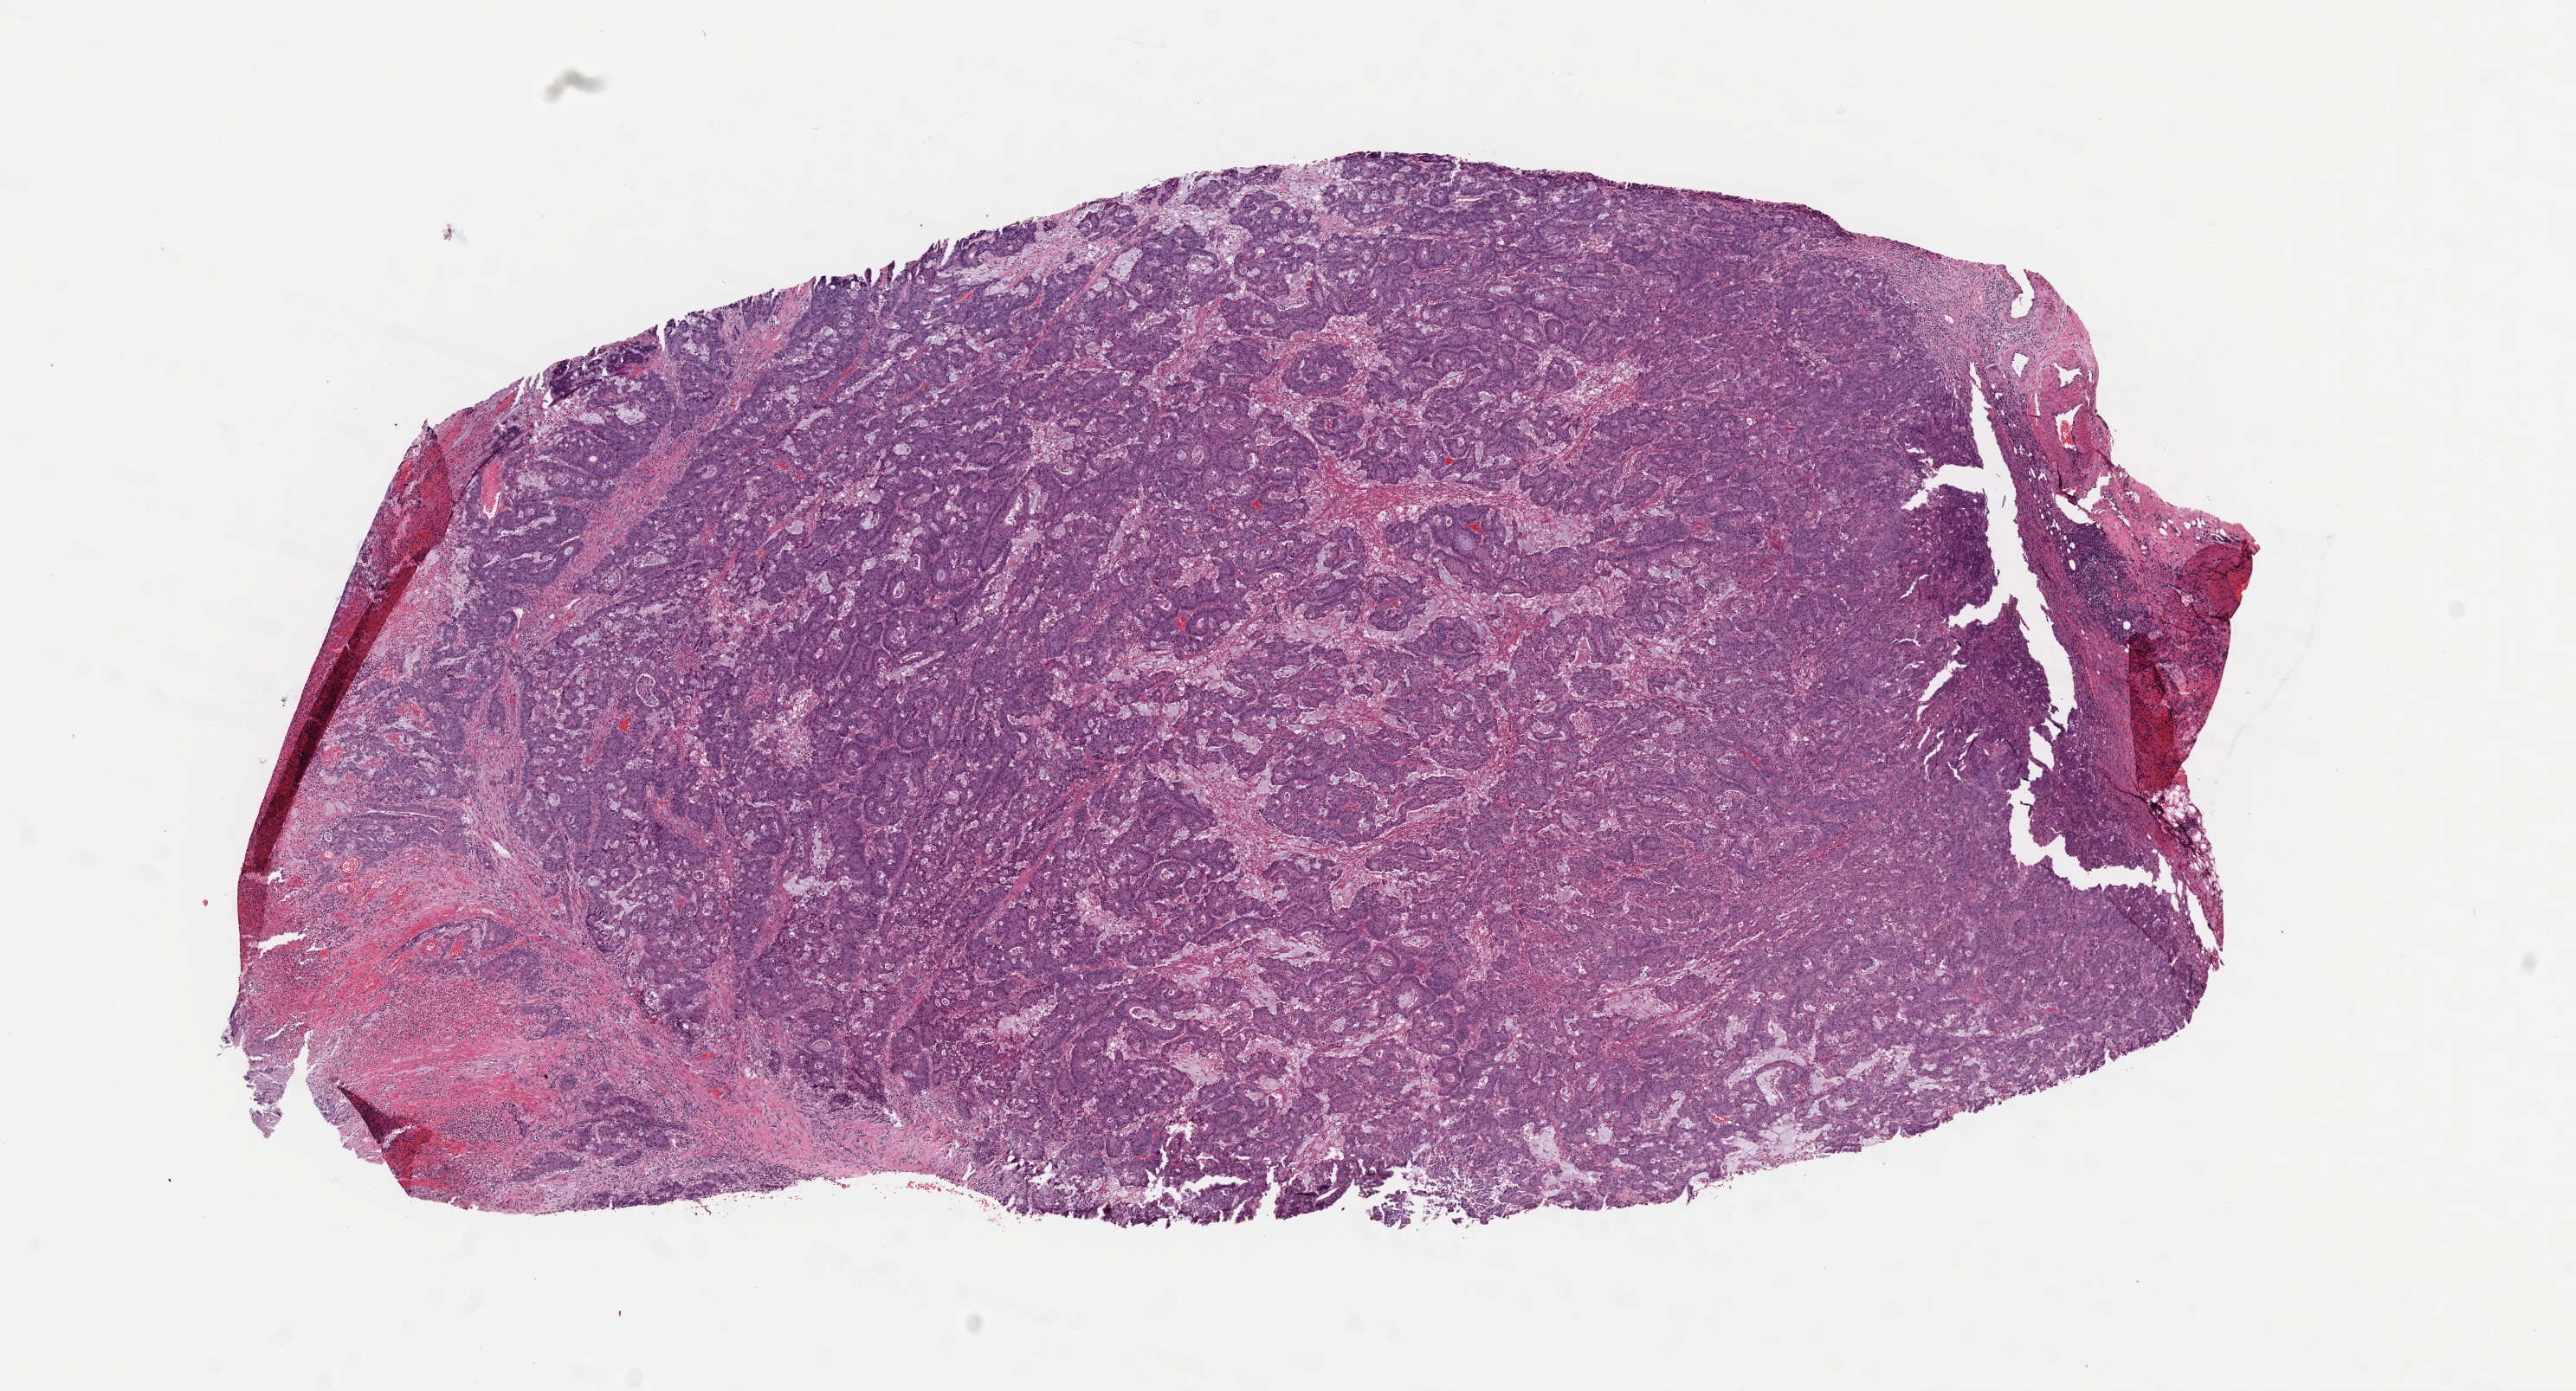
Whole-slide histology image, H&E-stained — low-resolution overview of the scanned area, about 11.7 x 6.3 mm (acquisition: 40x scan); frozen section; sample: primary tumour, colon. Patient: male, age at initial diagnosis 74 years. Composition of this section per pathologist review: tumour cells 97%, tumour nuclei 92%, normal cells 3%, stromal cells 0%, necrosis 0%. Infiltration values recorded for this section: lymphocyte infiltration 0%, monocyte infiltration 0%, neutrophil infiltration 0%.
Pathologic diagnosis: Mucinous adenocarcinoma (ascending colon). AJCC pathologic stage: IIA (7th edition). Lymph nodes positive (case pathology): 0 of 18 examined.